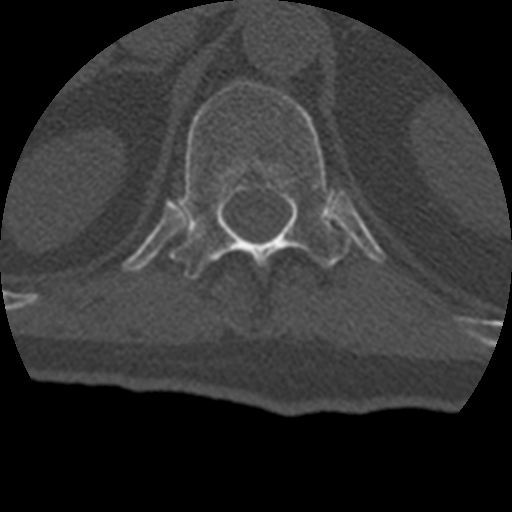
CT including the spine, one axial slice; reconstruction kernel STANDARD; 120 kVp; bone window (W 1800 / L 400 HU); 1.25 mm slice thickness; 512 × 512 image matrix. Patient age 69 years. From the clinical record (not read from this slice): primary cancer: prostate.
Annotated regions visible in this slice (semi-automatically segmented with operator editing):
- T12 vertebra: bounding box <172,81,351,279> (left, top, right, bottom; pixels)